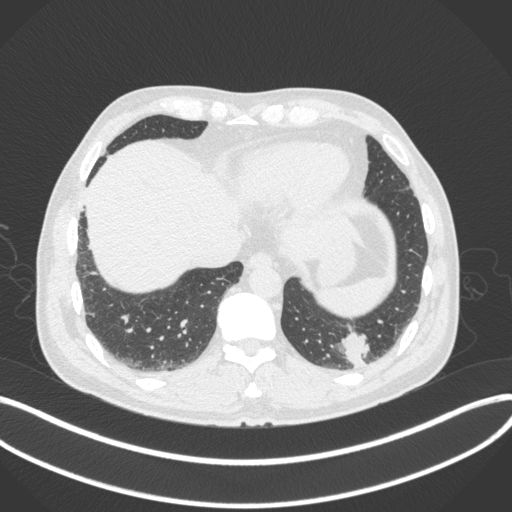
Chest CT, one axial slice; position 59 of 313 along the scan axis; reconstruction kernel B31f; 120 kVp; lung window (W 1500 / L -600 HU); 1 mm slice thickness; 512 × 512 image matrix, field of view 400 × 400 mm. Male patient, age 54 years. Case-level facts recorded for this patient, not image findings: clinical TNM (as recorded): T1c N0 M1; histopathological grade: G3.
Structures marked on this image (bounding box drawn by a radiologist):
- lung tumour (recorded histology: adenocarcinoma): bounding box (x1, y1, x2, y2) in pixels: (340, 331, 370, 368)